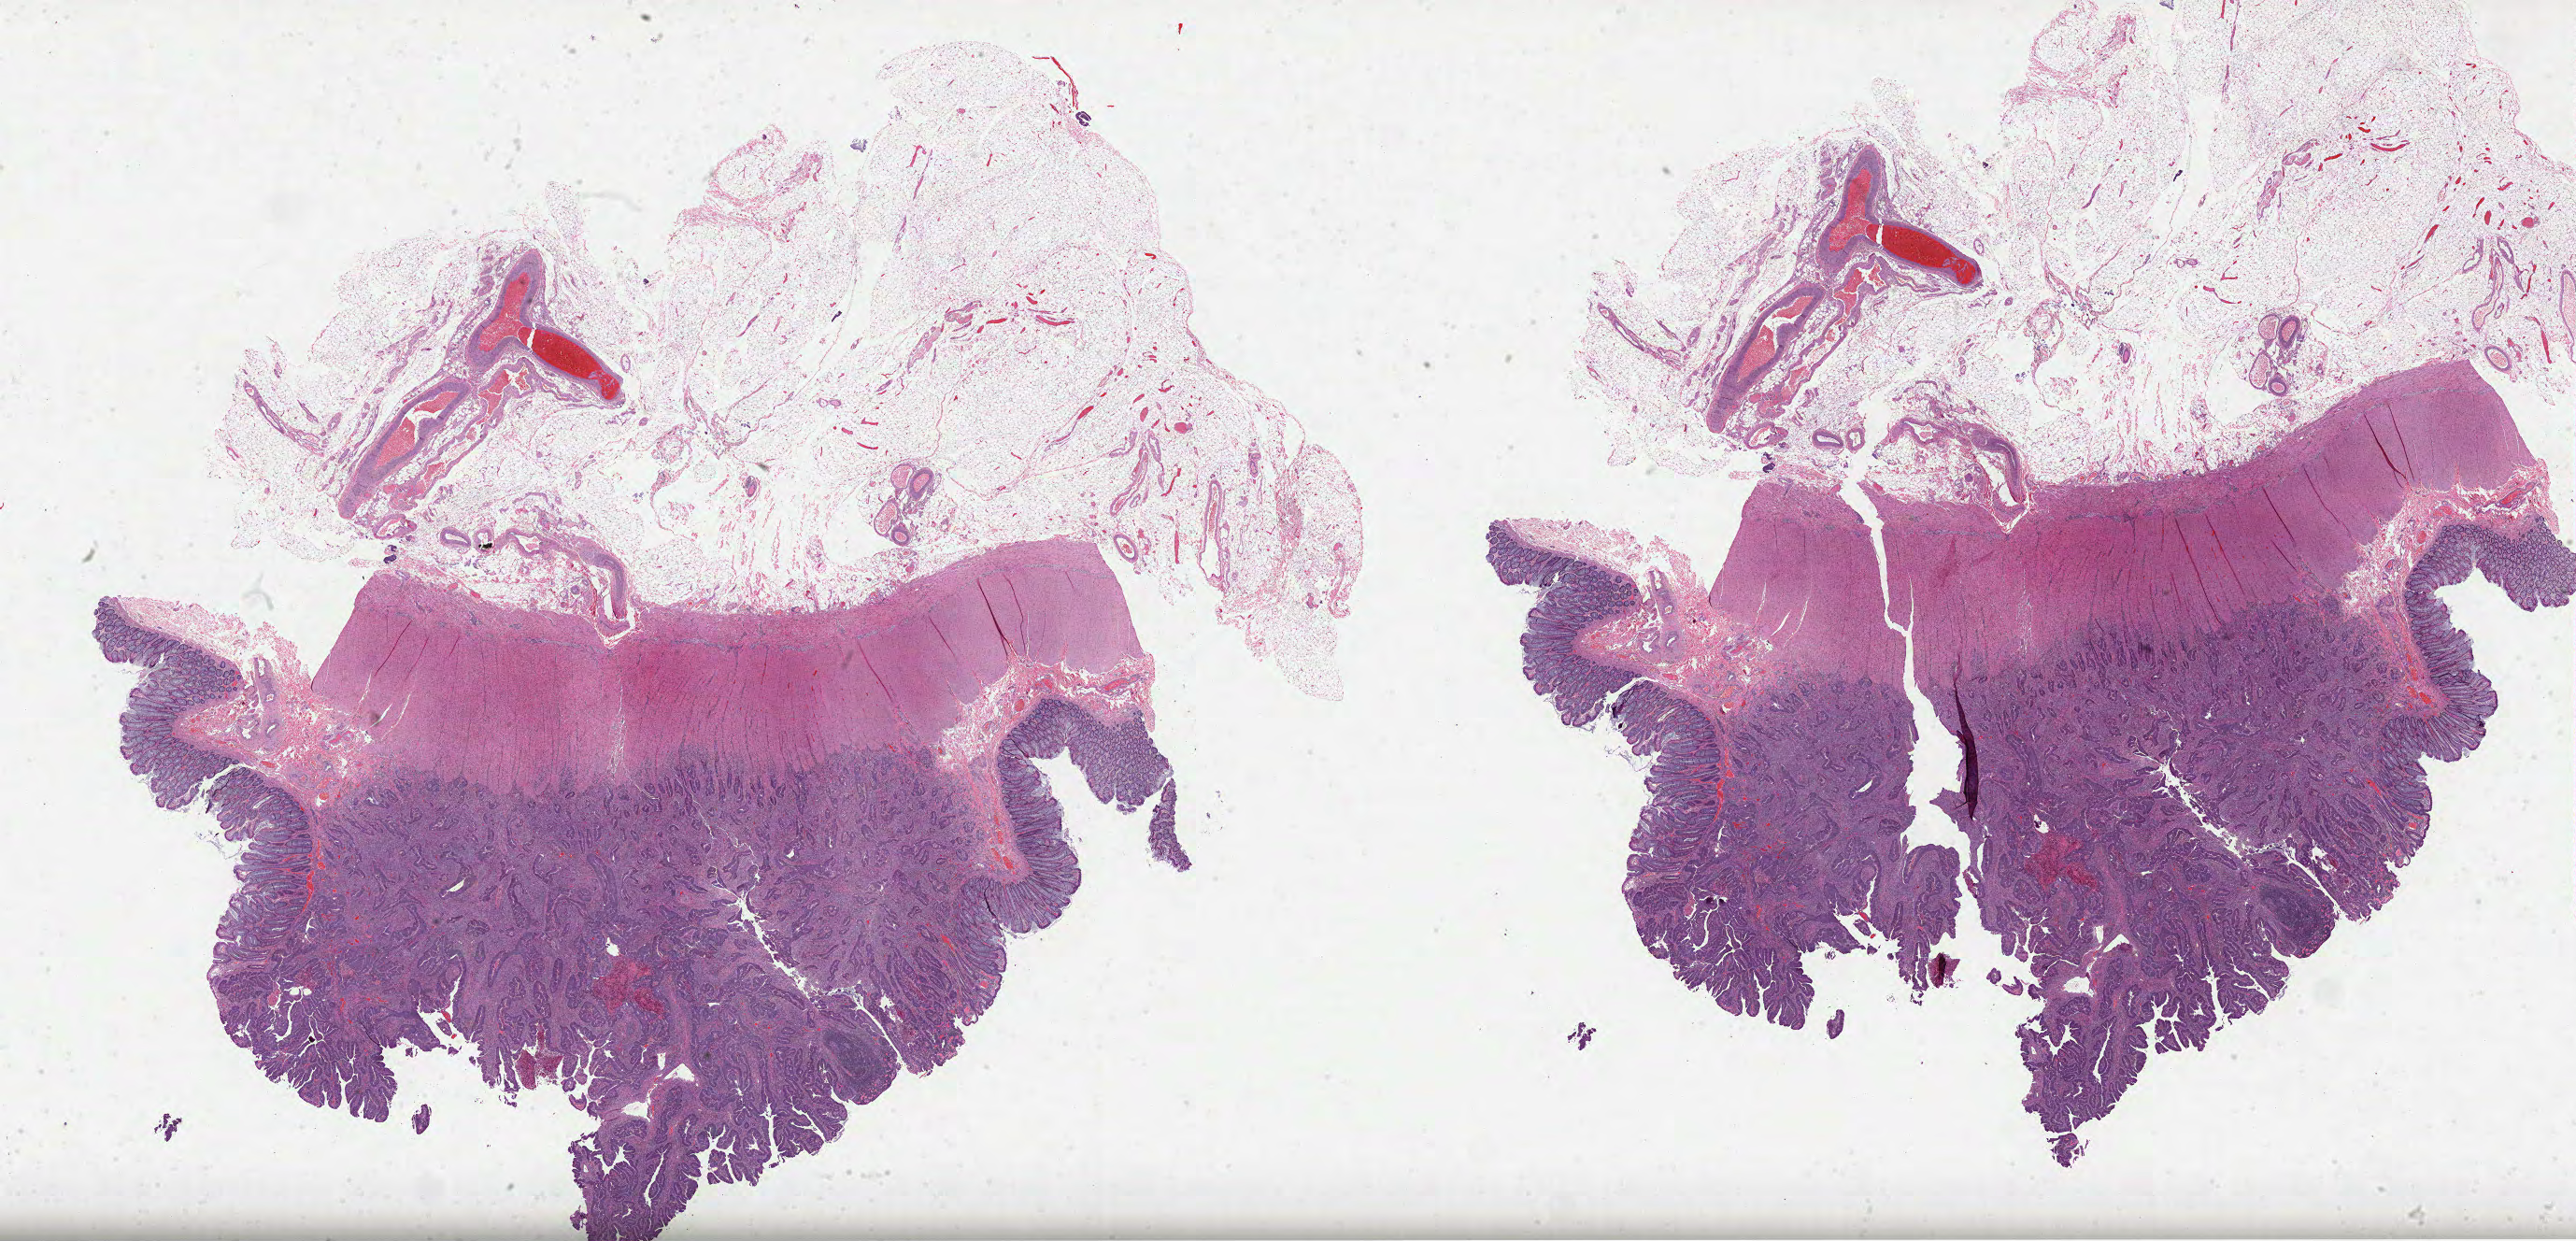
Whole-slide histology image, Hematoxylin and eosin (H&E) stained — whole scanned area (about 44.5 x 21.4 mm, acquisition: 40x scan) shown as a low-resolution overview, FFPE section, sample: primary tumour, rectum. Patient: female, age at initial diagnosis 31 years.
* lymph nodes positive (case pathology): 3 of 31 examined
* TNM: T2 N1b M0
* pathologic diagnosis: Adenocarcinoma, NOS (rectosigmoid junction)
* AJCC pathologic stage: IIIA (7th edition)